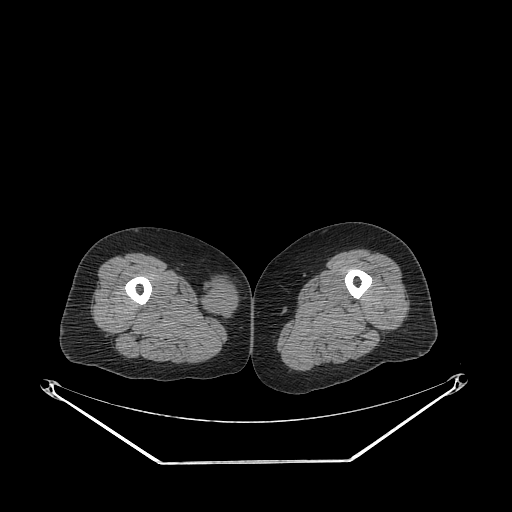
CT of an extremity soft-tissue mass (from a PET/CT study), one axial slice; slice 230 of 311 in the series (ordered by position); reconstruction kernel STANDARD; soft-tissue window (W 400 / L 40 HU); 3.75 mm slice thickness; 512 × 512 image matrix. Female patient. From the clinical record (not read from this slice): histological type: leiomyosarcoma; grade: intermediate; site of the primary tumour: parascapusular.
Structures marked on this image (expert contour drawn on MRI and transferred to this co-registered scan by the dataset authors):
- gross tumour volume including surrounding oedema: bounding box [x1, y1, x2, y2] px = [203, 274, 239, 321]
- gross tumour volume (mass): [203, 283, 239, 318]